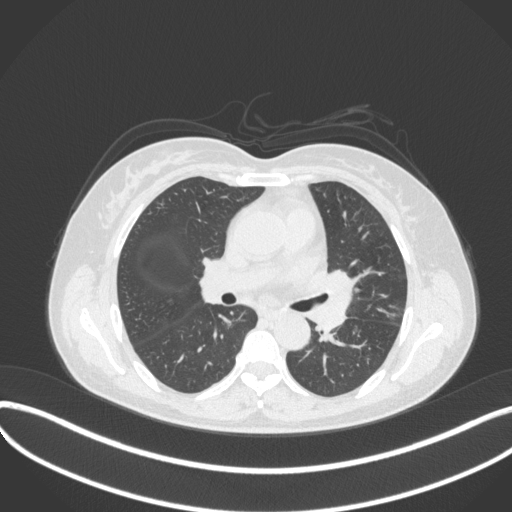
Chest CT, one axial slice. Position 198 of 373 along the scan axis. Reconstruction kernel B31f. 120 kVp. Lung window (W 1500 / L -600 HU). 512 × 512 image matrix, field of view 400 × 400 mm. Patient: female, 54 years. From the clinical record (not read from this slice): clinical TNM (as recorded): T2a N1 M0; histopathological grade: G3.
Annotated regions visible in this slice (bounding box drawn by a radiologist):
- lung tumour (recorded histology: small cell carcinoma): box from (x=308, y=269) to (x=358, y=336) px